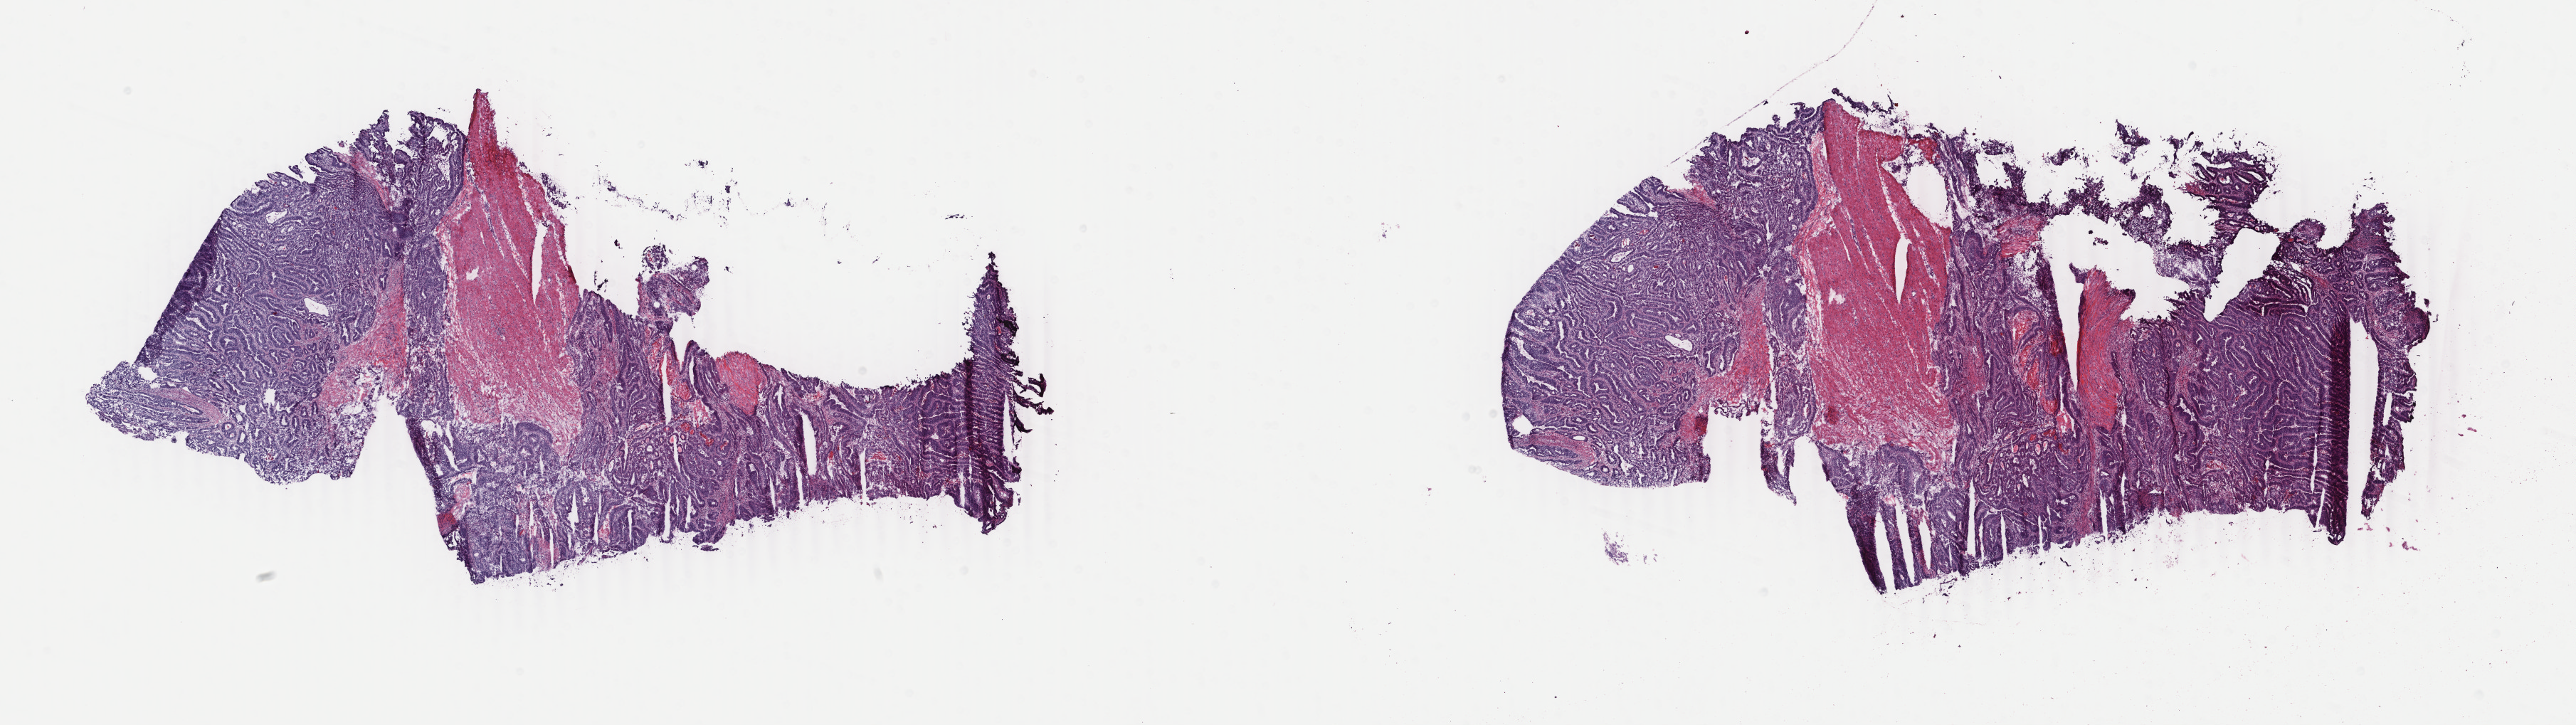
Whole-slide histology image, H&E-stained, a low-resolution overview of the entire scanned area, about 28.8 x 8.1 mm; frozen section; sample: primary tumour, colon. Patient: female, age at initial diagnosis 80 years. Composition of this section per pathologist review: tumour cells 80%, tumour nuclei 80%, normal cells 0%, stromal cells 17%, necrosis 3%. Infiltration values recorded for this section: lymphocyte infiltration 2%, monocyte infiltration 0%, neutrophil infiltration 0%.
Lymph nodes positive (case pathology): 2 of 14 examined. Pathologic diagnosis: Adenocarcinoma, NOS (sigmoid colon). AJCC pathologic stage: III.